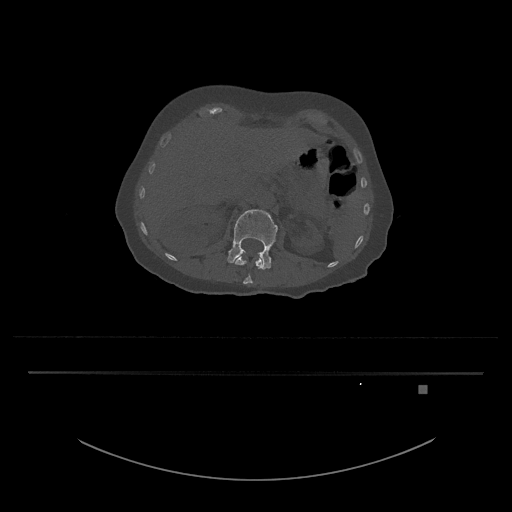
CT including the spine, one axial slice. Position 514 of 797 along the scan axis. Reconstruction kernel Br40s/3. 120 kVp. Bone window (W 1800 / L 400 HU). 0.5 mm slice thickness. 512 × 512 image matrix, field of view 500 × 500 mm. Female patient, age 57 years. From the clinical record (not read from this slice): primary cancer: cervical.
Outlined on this slice (semi-automatically segmented with operator editing):
- L1 vertebra: bounding box <235,253,263,284> (left, top, right, bottom; pixels)